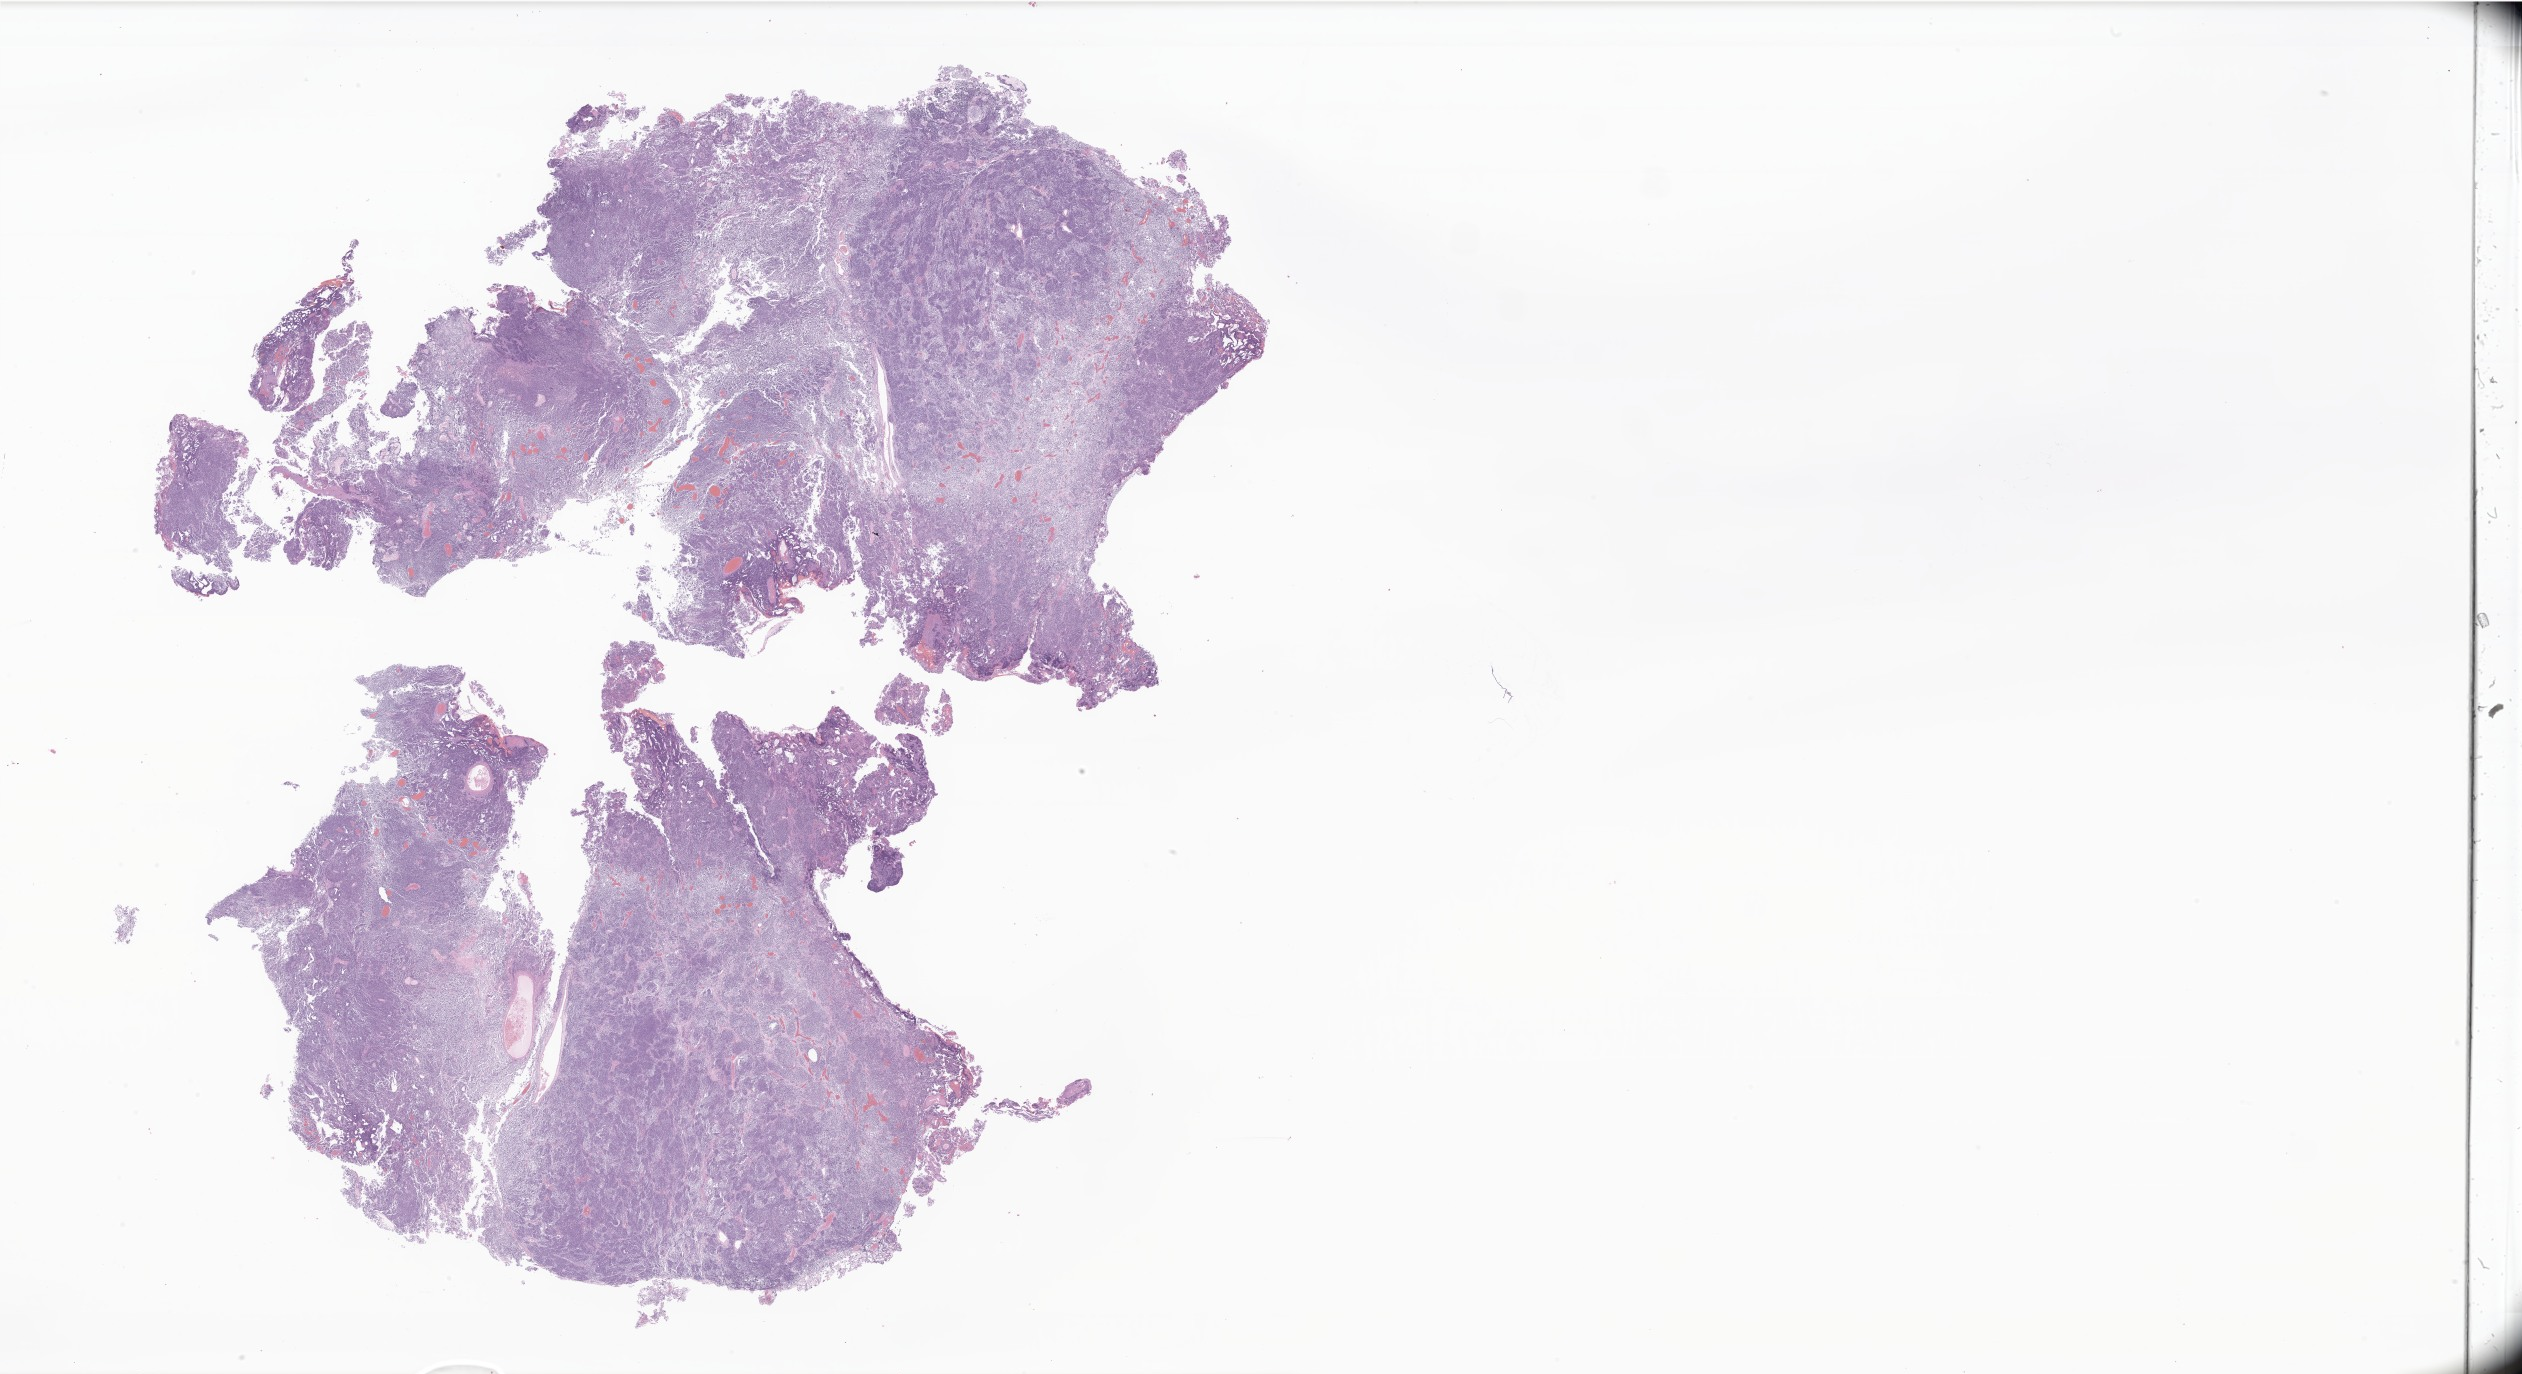
Whole-slide image, H&E stain of tumor tissue from the brain — shown as a low-resolution overview of the whole scanned area (about 42.5 x 23.2 mm). Formalin-fixed, paraffin-embedded (FFPE) tissue. Patient: male, age 105 months.
- diagnosis: Medulloblastoma, NOS